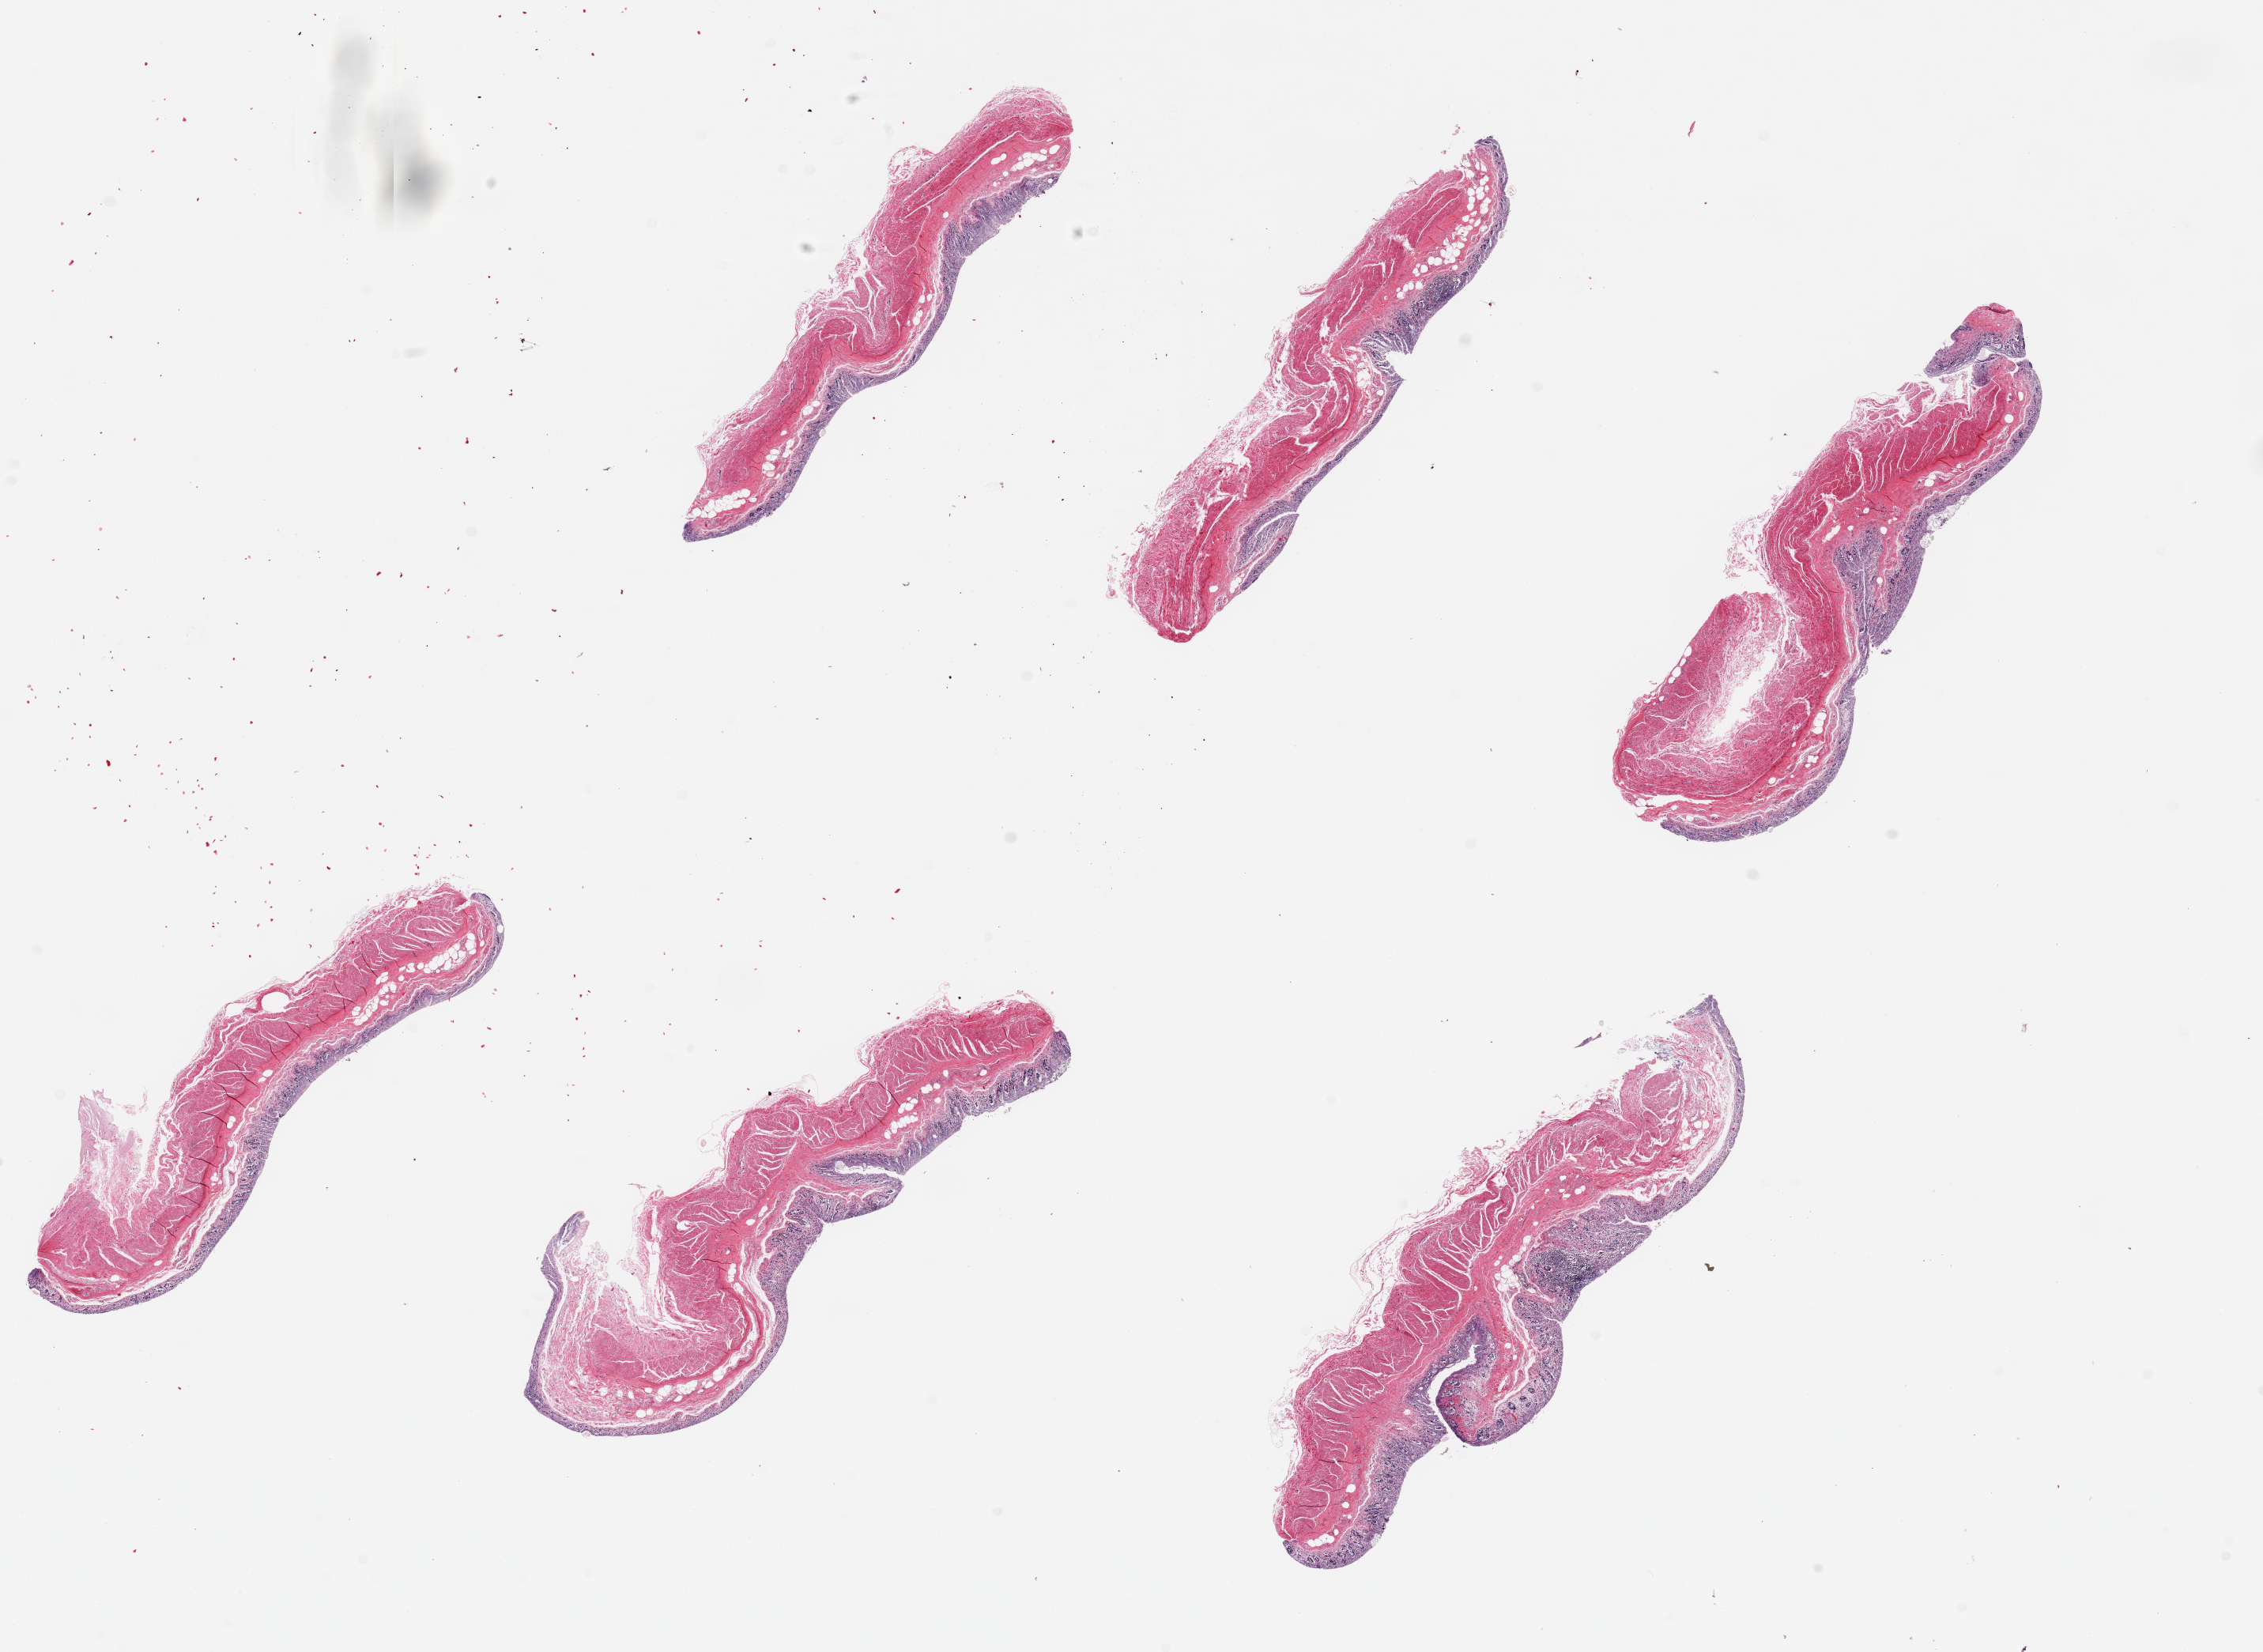
Digitized hematoxylin and eosin (H&E)-stained section — shown as a low-resolution overview of the whole scanned area (about 22.6 x 16.5 mm); PAXgene-fixed, paraffin-embedded tissue; section of transverse colon (target tissue); donor tissue sample. Male donor.
• reviewer comment on this tissue sample: 6 pieces, up to 7x2mm; mucosa = 3; muscularis = 2 (autolysis)